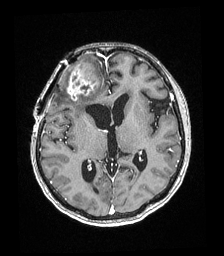
Brain MRI from a brain-tumour surgery series, one axial slice; position 98 of 192 along the scan axis; T1-weighted post-contrast; 1 mm slice thickness; 224 × 256 image matrix. From the clinical record (not read from this slice): histopathology: Astrocytoma; WHO grade: 4; IDH mutation: yes.
Outlined on this slice (expert manual segmentation):
- tumour: box from (x=67, y=59) to (x=99, y=100) px